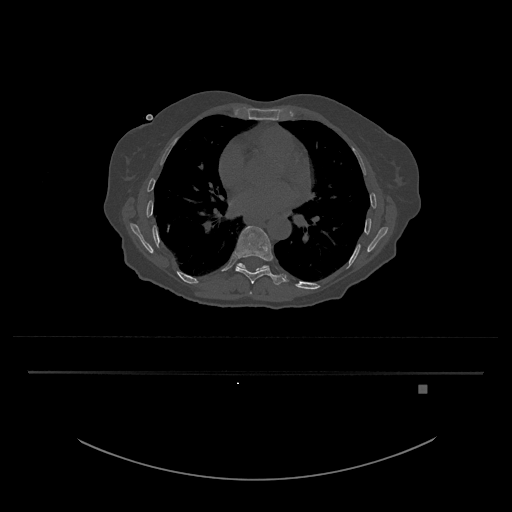
CT including the spine, one axial slice; position 752 of 797 along the scan axis; reconstruction kernel Br40s/3; 120 kVp; bone window (W 1800 / L 400 HU); 512 × 512 image matrix, field of view 500 × 500 mm. Female patient, age 57 years. Case-level facts recorded for this patient, not image findings: primary cancer: cervical.
Annotated regions visible in this slice (semi-automatic segmentation, software-assisted and operator-edited):
- T10 vertebra: bounding box (x1, y1, x2, y2) in pixels: (236, 263, 269, 272)
- T8 vertebra: (249, 291, 252, 294)
- T9 vertebra: (235, 226, 285, 285)